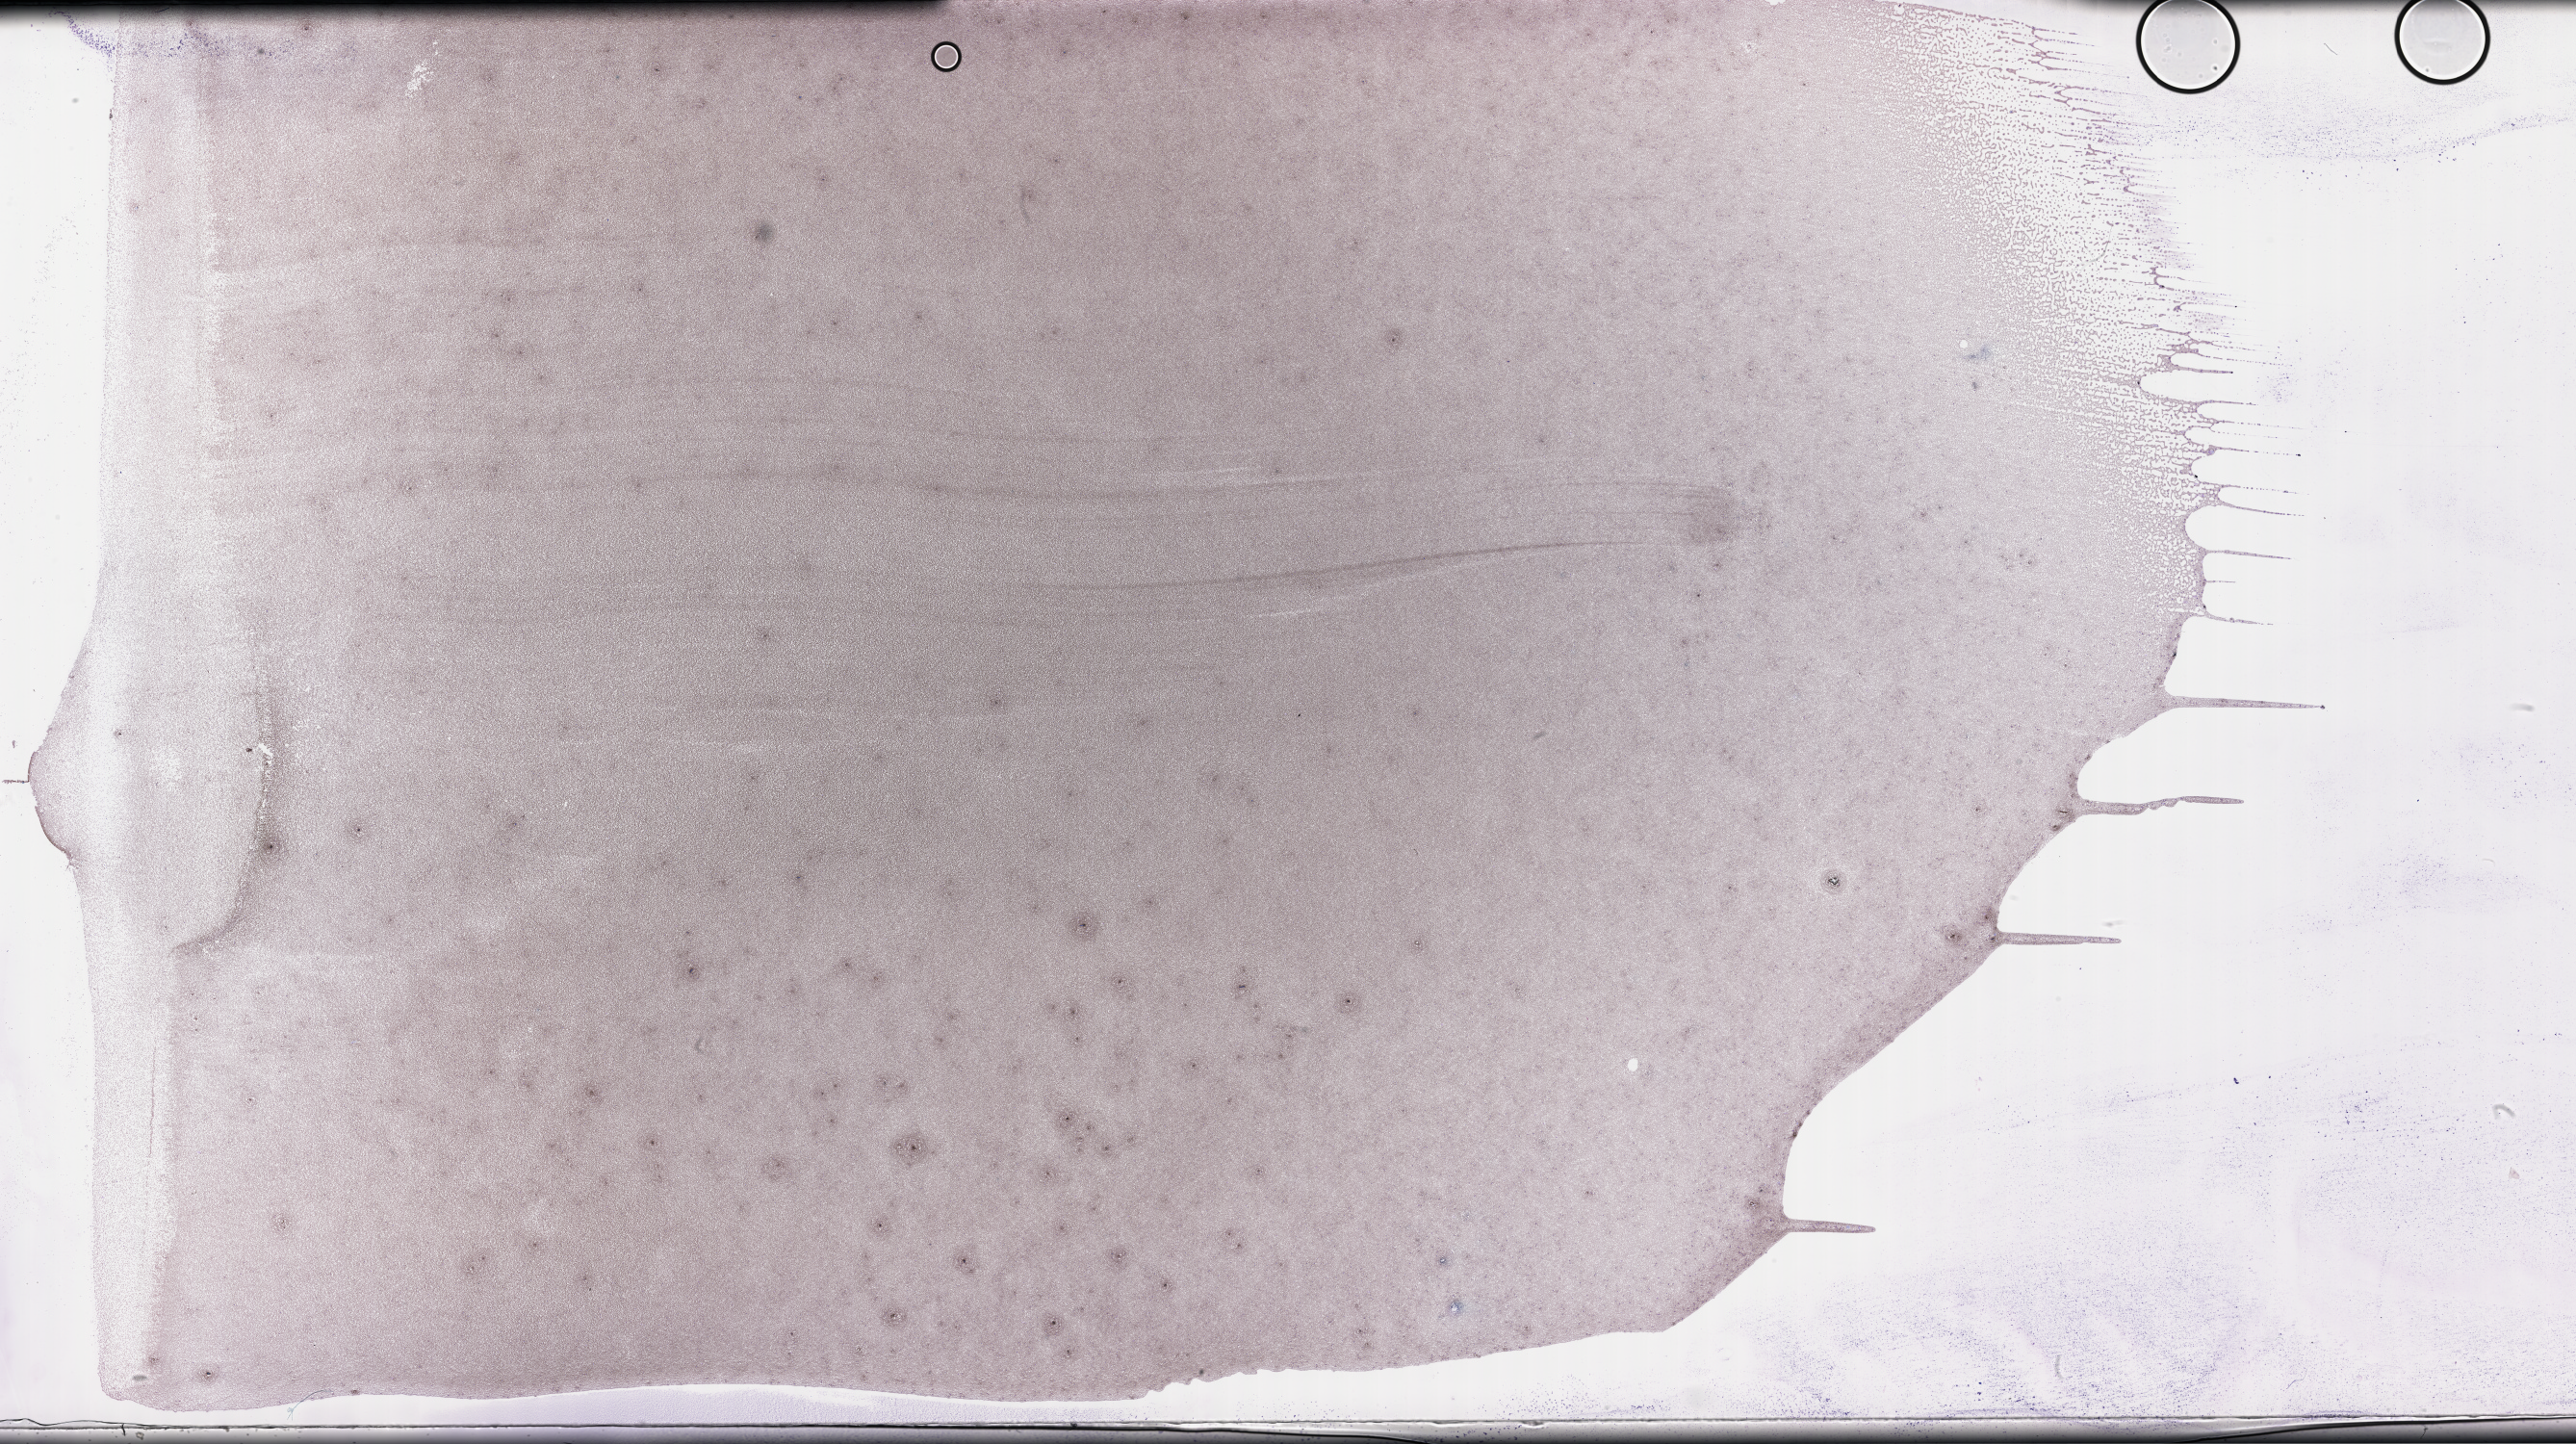
Wright-Giemsa-stained whole blood smear, whole-slide image — shown as a low-resolution overview of the whole scanned area (about 43.2 x 24.2 mm); specimen time point: collected on treatment. Male patient.
From a patient with: Plasma Cell Myeloma.